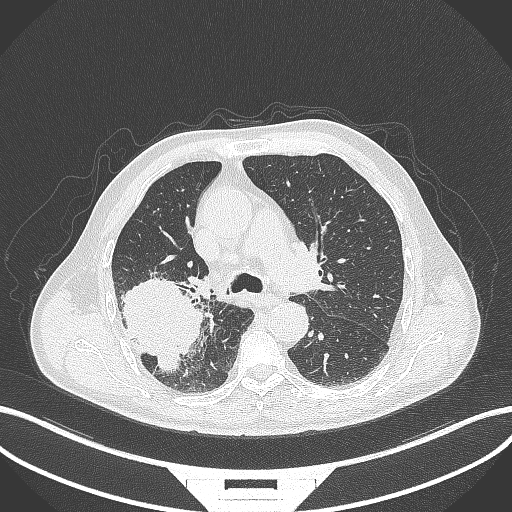
Chest CT, one axial slice; position 264 of 429 along the scan axis; reconstruction kernel B70f; 120 kVp; lung window (W 1500 / L -600 HU); 512 × 512 image matrix. Patient: male, 72 years. Case-level facts recorded for this patient, not image findings: clinical TNM (as recorded): T3 N2 M0.
Annotated regions visible in this slice (rectangle marked by the reading radiologist):
- lung tumour (recorded histology: adenocarcinoma): bounding box (x1, y1, x2, y2) in pixels: (113, 276, 203, 375)